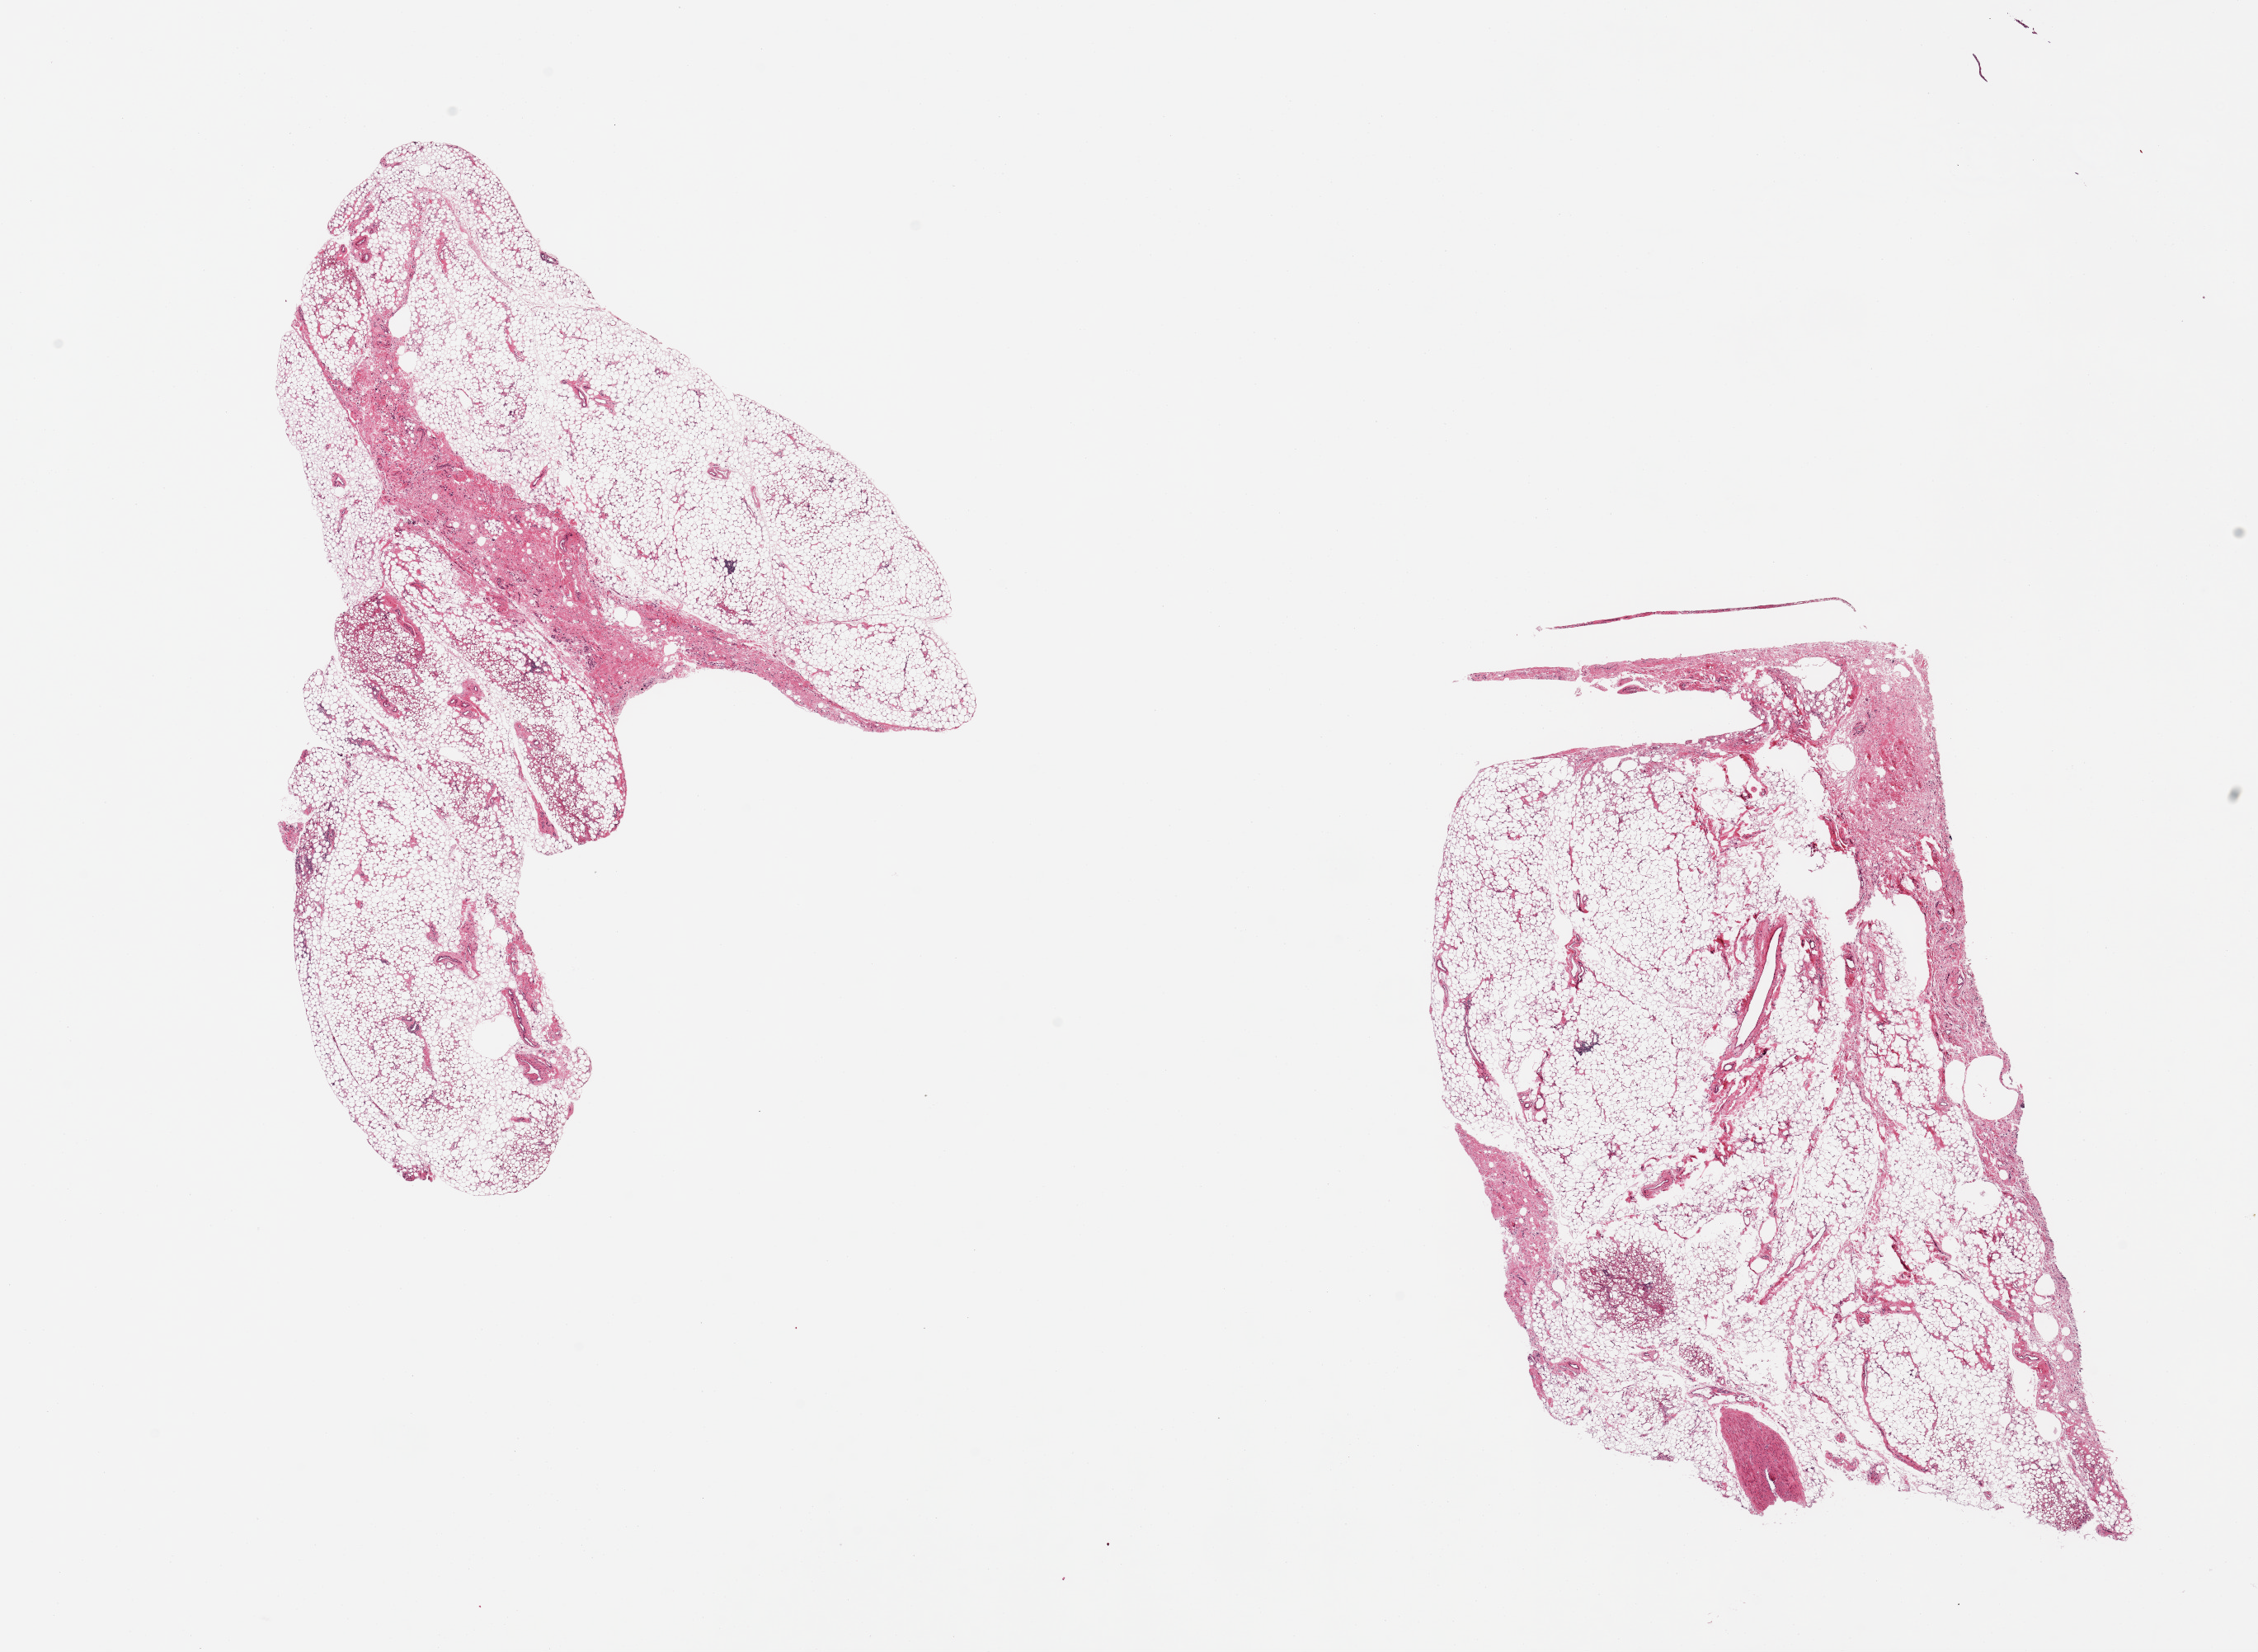
Whole-slide image, haematoxylin and eosin stain, low-resolution overview of the scanned area, about 21.7 x 15.8 mm (slide scanned at 20x). PAXgene-fixed paraffin-embedded (PFPE) section. Sampled site (target tissue): adrenal gland. Donor tissue sample.
Review note (as recorded): 2 pieces; no adrenal, all fat.